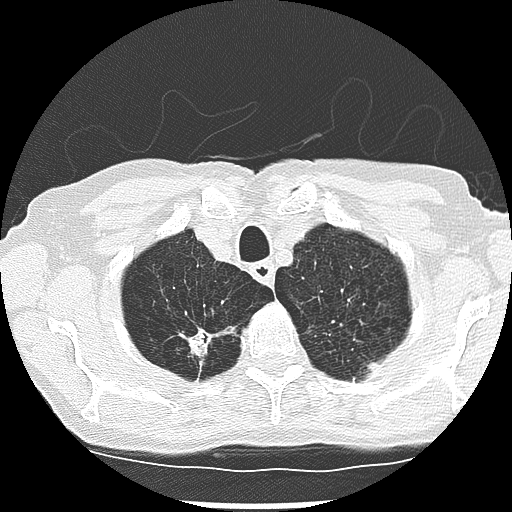
Low-dose screening chest CT, one axial slice. Position 236 of 265 along the scan axis. Reconstruction kernel LUNG. Lung window (W 1500 / L -600 HU). 512 × 512 image matrix.
Structures marked on this image (manually delineated by an expert):
- lesion 2 (tumor, upper lobe of right lung): bounding box (x1, y1, x2, y2) in pixels: (180, 328, 215, 358)